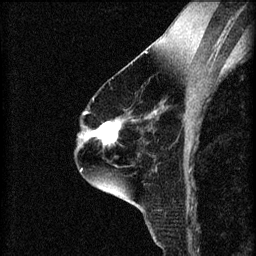
Breast MRI (dynamic contrast-enhanced), one sagittal slice. Slice 41 of 60 in the series (ordered by position). 3 images stored at this slice position (order not interpretable as contrast timing). 1.5 T. TE 4.2 ms, TR 8.2 ms. 2 mm slice thickness. 256 × 256 image matrix, field of view 180 × 180 mm. Patient: female, 60 years.
Outlined on this slice (semi-automatic segmentation, software-assisted and operator-edited):
- analysis volume of interest (the breast-tissue region the enhancement analysis was run in; not a lesion): box from (x=89, y=116) to (x=127, y=149) px
- tumour enhancement mask (voxels above the 70 % enhancement threshold inside the analysis volume of interest): (x=90, y=120)–(x=121, y=145)